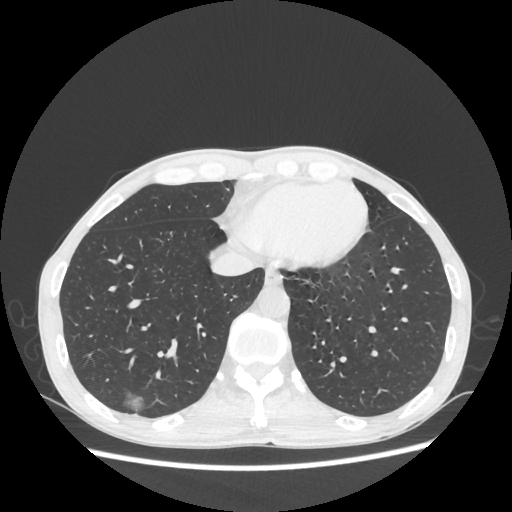
Chest CT, one axial slice. Position 75 of 270 along the scan axis. 100 kVp. Lung window (W 1500 / L -600 HU). 1.25 mm slice thickness. 512 × 512 image matrix. Patient: male, 60 years. From the clinical record (not read from this slice): clinical TNM (as recorded): T1c N0 M0.
Structures marked on this image (rectangle marked by the reading radiologist):
- lung tumour (recorded histology: adenocarcinoma): bounding box [x1, y1, x2, y2] px = [120, 386, 154, 420]